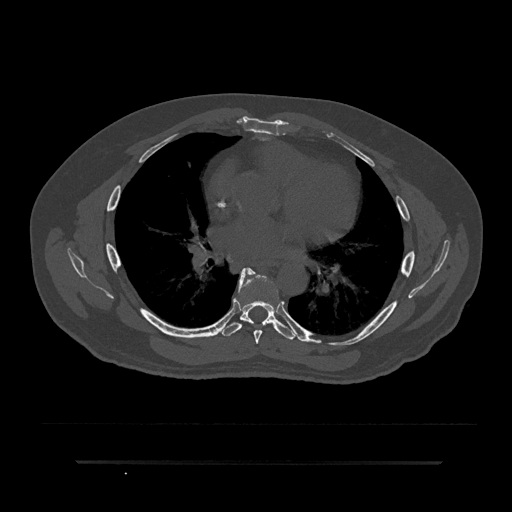
CT including the spine, one axial slice; slice 501 of 797 in the series (ordered by position); reconstruction kernel Br40s/3; 120 kVp; bone window (W 1800 / L 400 HU); 0.5 mm slice thickness; 512 × 512 image matrix, field of view 464 × 464 mm. Male patient, age 59 years. Case-level facts recorded for this patient, not image findings: primary cancer: bile ducts.
Annotated regions visible in this slice (semi-automatic segmentation, software-assisted and operator-edited):
- T6 vertebra: bounding box (x1, y1, x2, y2) in pixels: (239, 268, 273, 344)
- T7 vertebra: (222, 268, 297, 340)